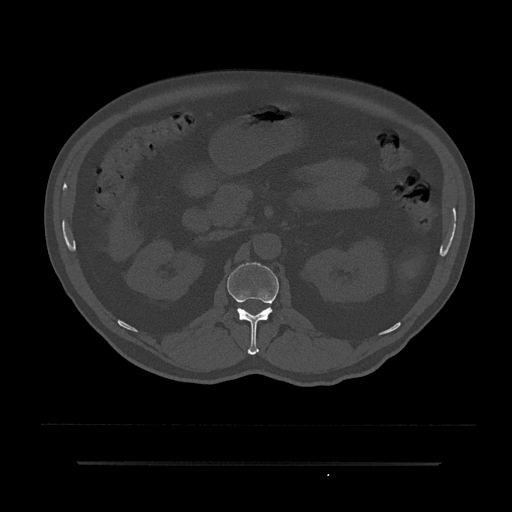
CT including the spine, one axial slice; 120 kVp; bone window (W 1800 / L 400 HU); 0.5 mm slice thickness; 512 × 512 image matrix, field of view 464 × 464 mm. Male patient, age 59 years. Case-level facts recorded for this patient, not image findings: primary cancer: bile ducts.
Outlined on this slice (semi-automatically segmented with operator editing):
- L1 vertebra: bounding box [x1, y1, x2, y2] px = [228, 263, 283, 355]